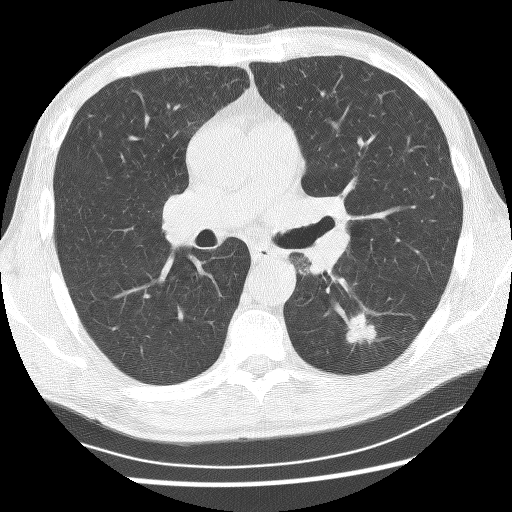
Low-dose screening chest CT, one axial slice. Position 143 of 253 along the scan axis. Lung window (W 1500 / L -600 HU). 2.5 mm slice thickness. 512 × 512 image matrix, field of view 340 × 340 mm.
Structures marked on this image (outlined manually by an expert reader):
- lesion 1 (tumor, lower lobe of left lung): bounding box [x1, y1, x2, y2] px = [346, 313, 376, 344]